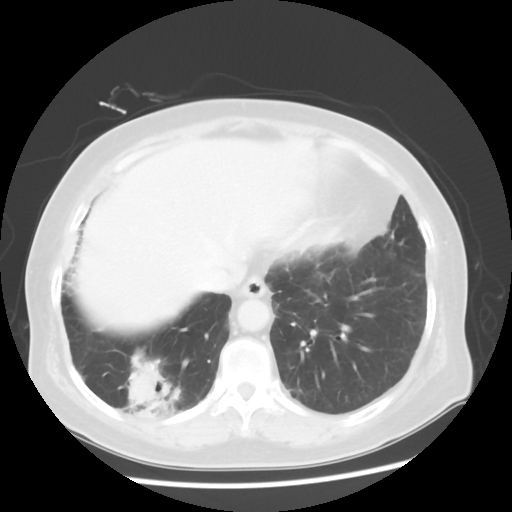
Chest CT, one axial slice; position 15 of 56 along the scan axis; reconstruction kernel STANDARD; lung window (W 1500 / L -600 HU); 5 mm slice thickness; 512 × 512 image matrix. Female patient, age 64 years. Case-level facts recorded for this patient, not image findings: clinical TNM (as recorded): Tis N0 M0.
Annotated regions visible in this slice (rectangle marked by the reading radiologist):
- lung tumour (recorded histology: adenocarcinoma): bounding box (x1, y1, x2, y2) in pixels: (116, 344, 187, 435)